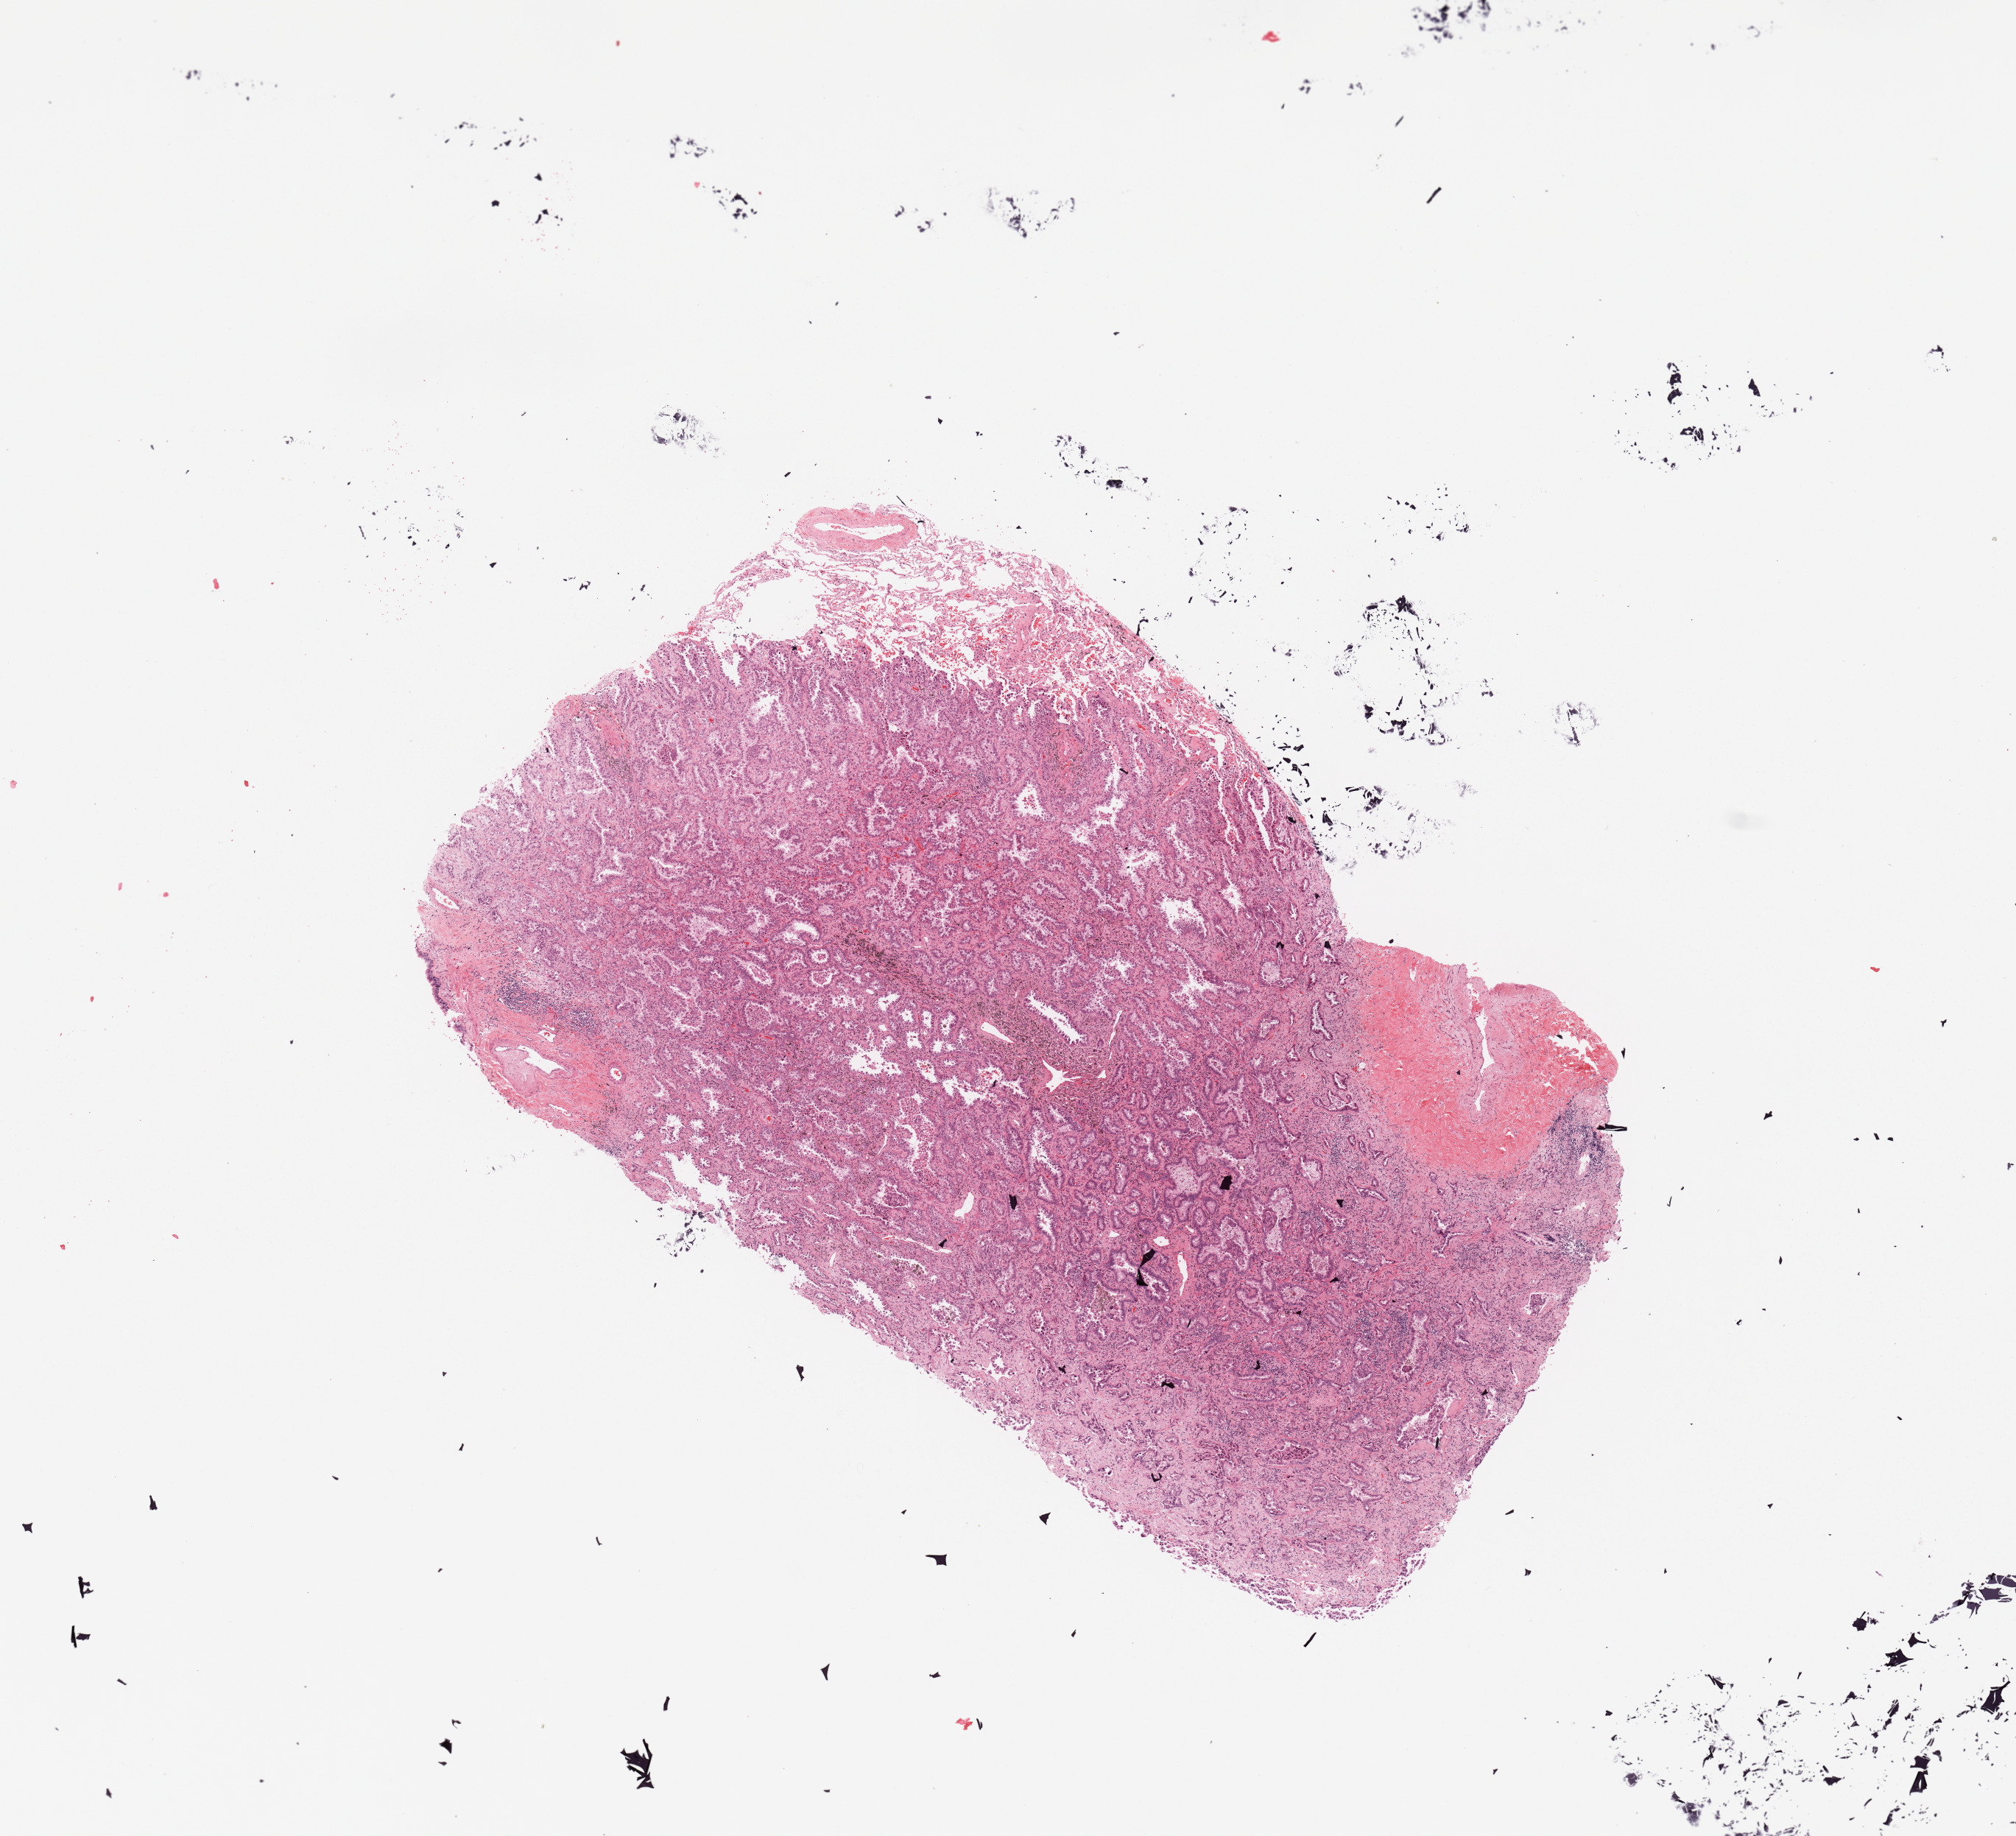
Hematoxylin and eosin (H&E) stained whole-slide image — a low-resolution overview of the entire scanned area, about 10.8 x 9.9 mm (from a 20x scan); tumour tissue sample, sampled site: lung. Female, 68 y/o. Histologic grade: G2 (moderately differentiated). Composition of this section per pathologist review: tumour nuclei 80%, necrosis 2%.
AJCC pathologic stage: IA. Diagnosis: Adenocarcinoma, NOS. Primary tumour site (as recorded): right upper lobe.